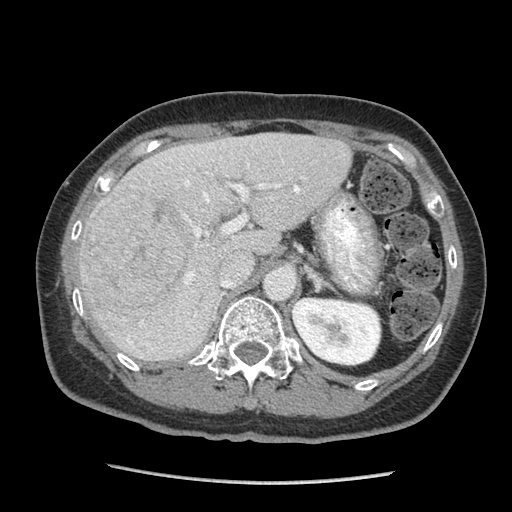
Contrast-enhanced abdominal CT (liver protocol), one axial slice. Slice 54 of 105 in the series (ordered by position). 140 kVp. Soft-tissue window (W 400 / L 40 HU). 512 × 512 image matrix, field of view 340 × 340 mm. From the clinical record (not read from this slice): diagnosis: hepatocellular carcinoma (patient treated with transarterial chemoembolisation; whether this scan precedes or follows treatment is not stated here); TNM stage (as recorded): Stage-I; Child-Pugh class: A.
Outlined on this slice (semi-automatically segmented with operator editing):
- liver parenchyma outside the tumour (the mass and vessels are separate outlines, so this box may not span the whole liver): bounding box <78,132,352,360> (left, top, right, bottom; pixels)
- mass: <83,191,202,311>
- liver vessels: <127,164,300,345>